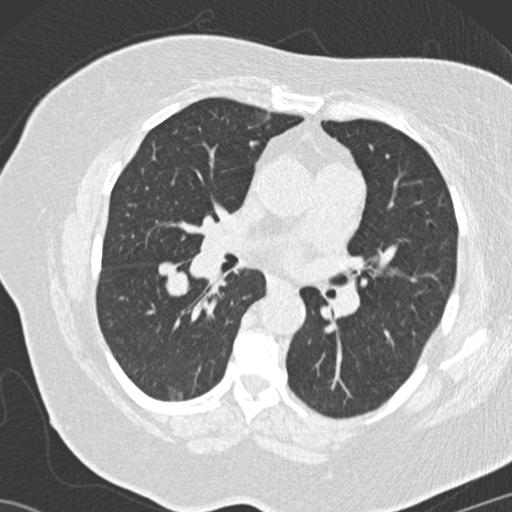
Low-dose screening chest CT, one axial slice. Slice 75 of 146 in the series (ordered by position). Reconstruction kernel B30f. Lung window (W 1500 / L -600 HU). 512 × 512 image matrix.
Structures marked on this image (manually delineated by an expert):
- lesion 4 (tumor, lower lobe of right lung): box from (x=158, y=264) to (x=190, y=298) px